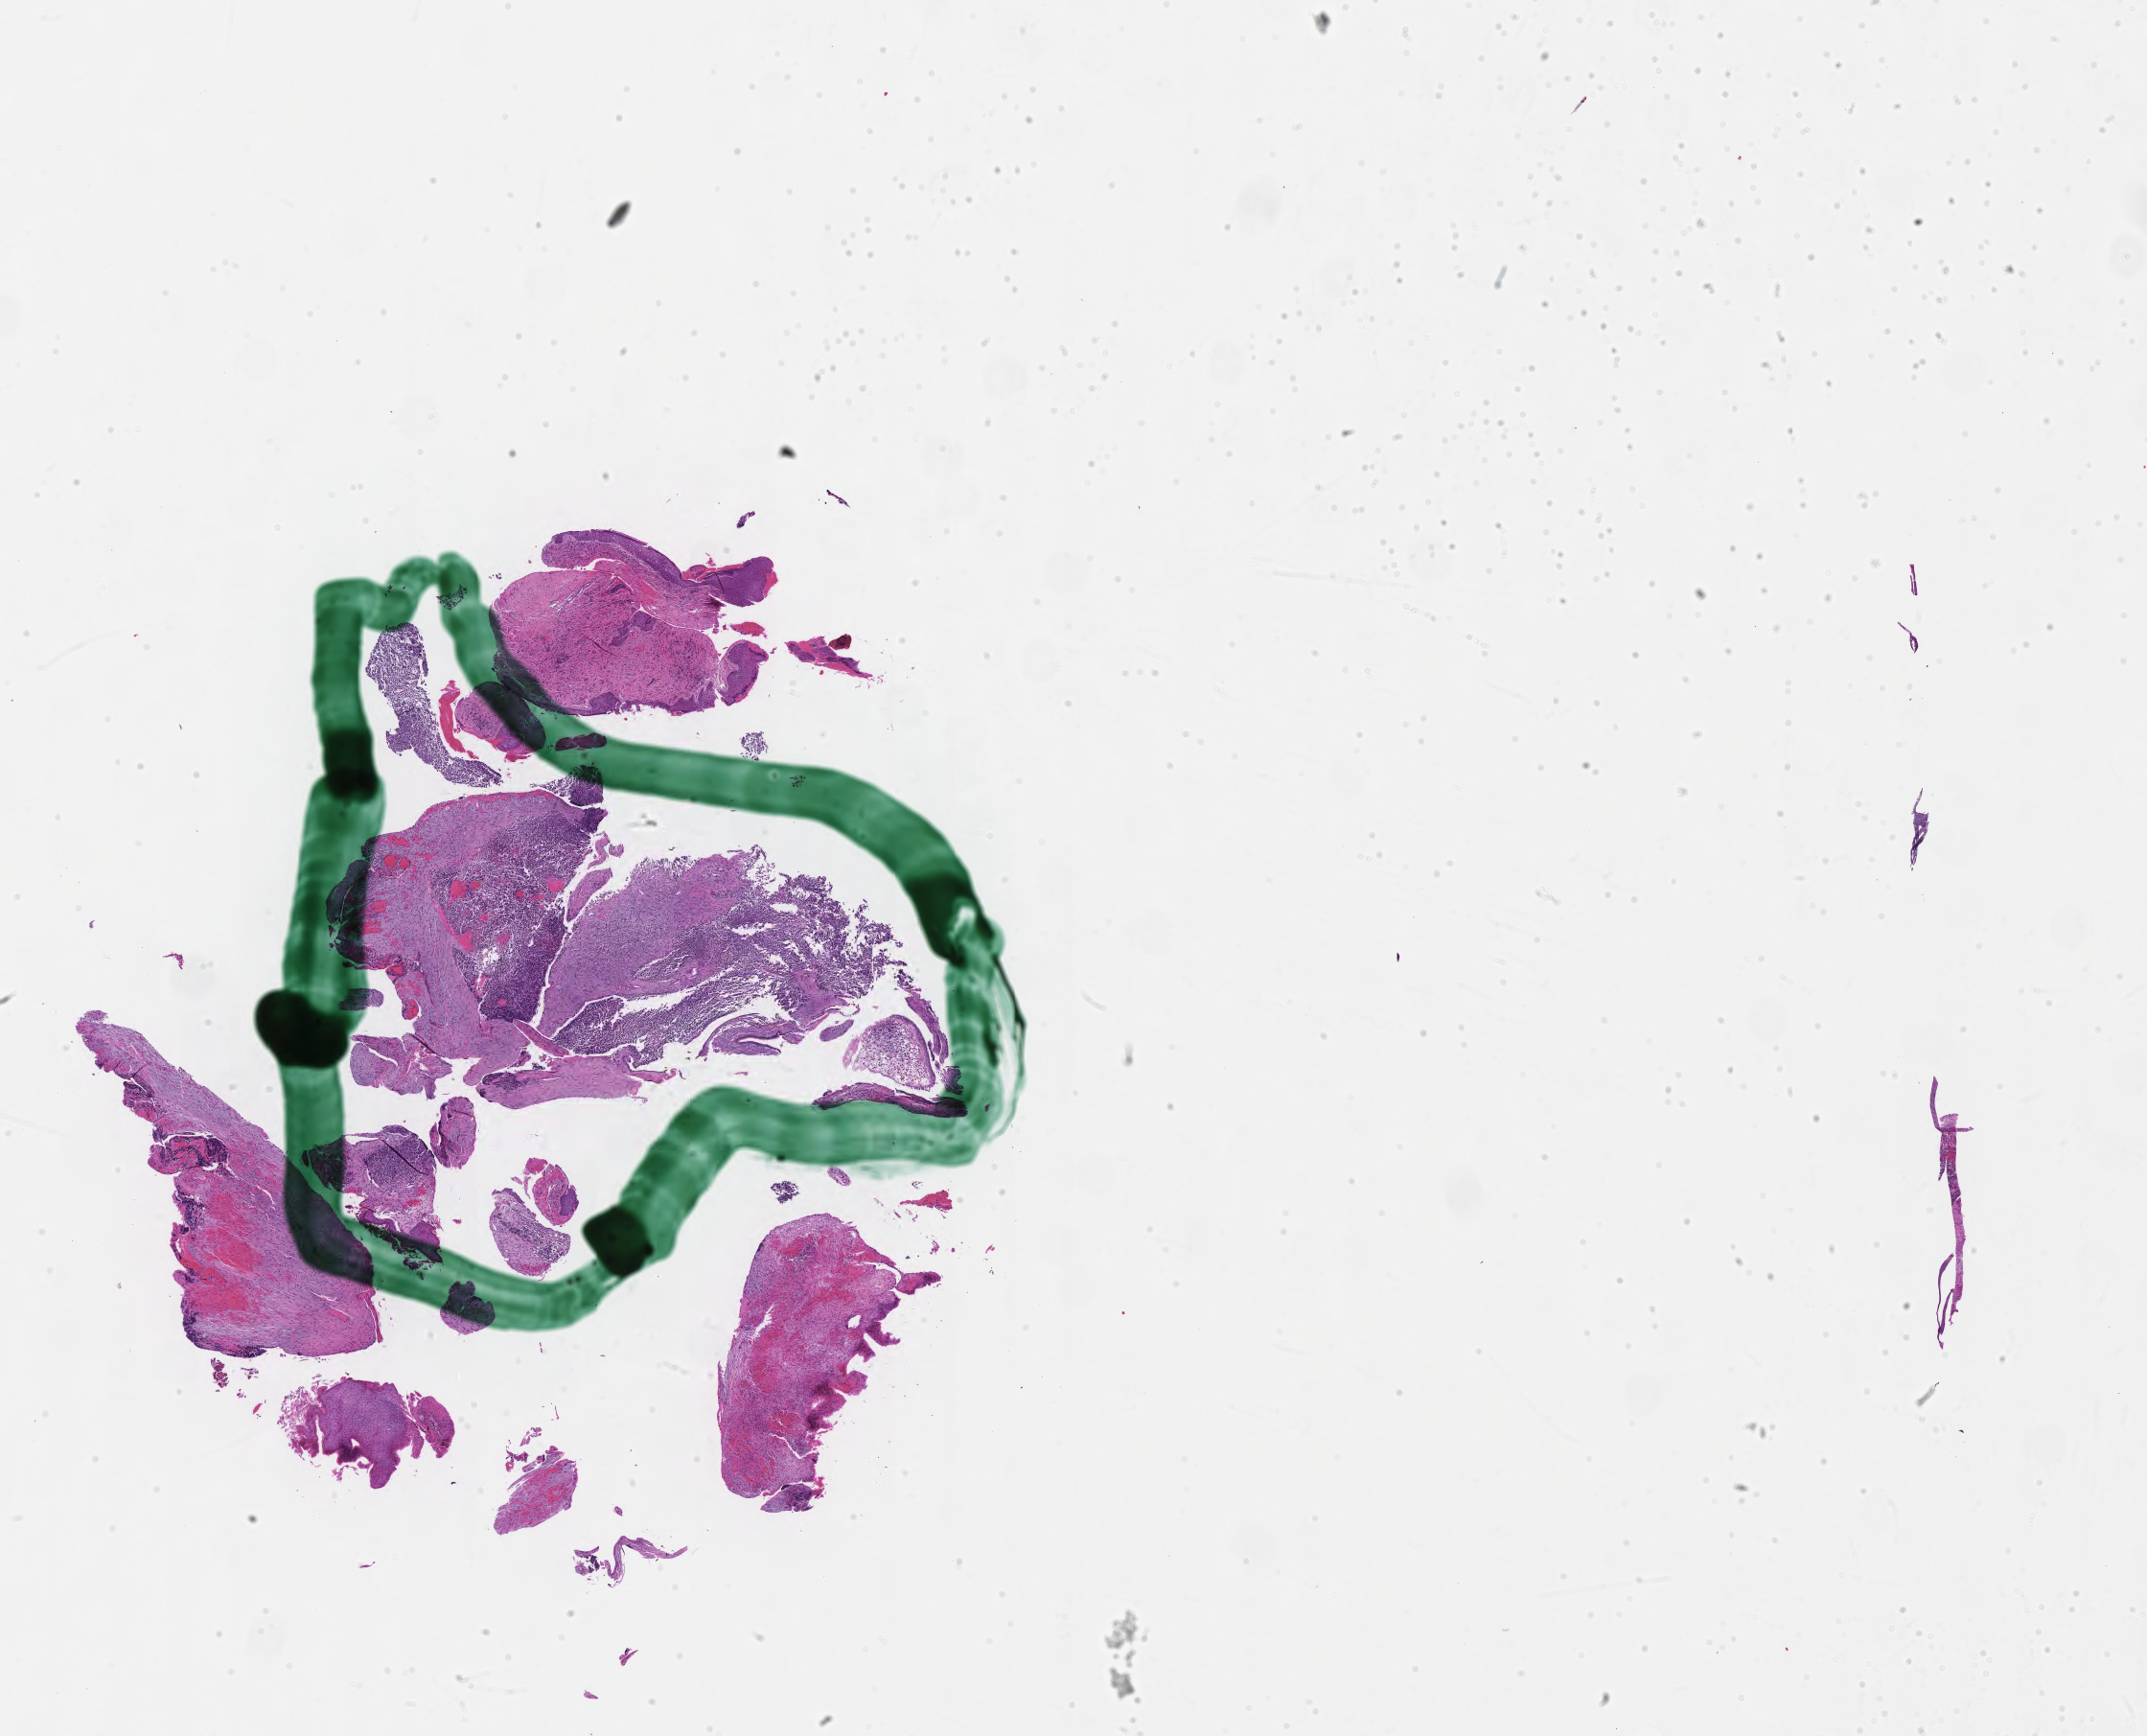
Whole-slide image, hematoxylin and eosin (H&E) stain of tumor tissue from the middle ear — shown as a low-resolution overview of the whole scanned area (about 18.1 x 14.6 mm); formalin-fixed, paraffin-embedded (FFPE) tissue. Patient: male, age 84 months (7 years).
Diagnosis: Rhabdomyosarcoma, NOS.